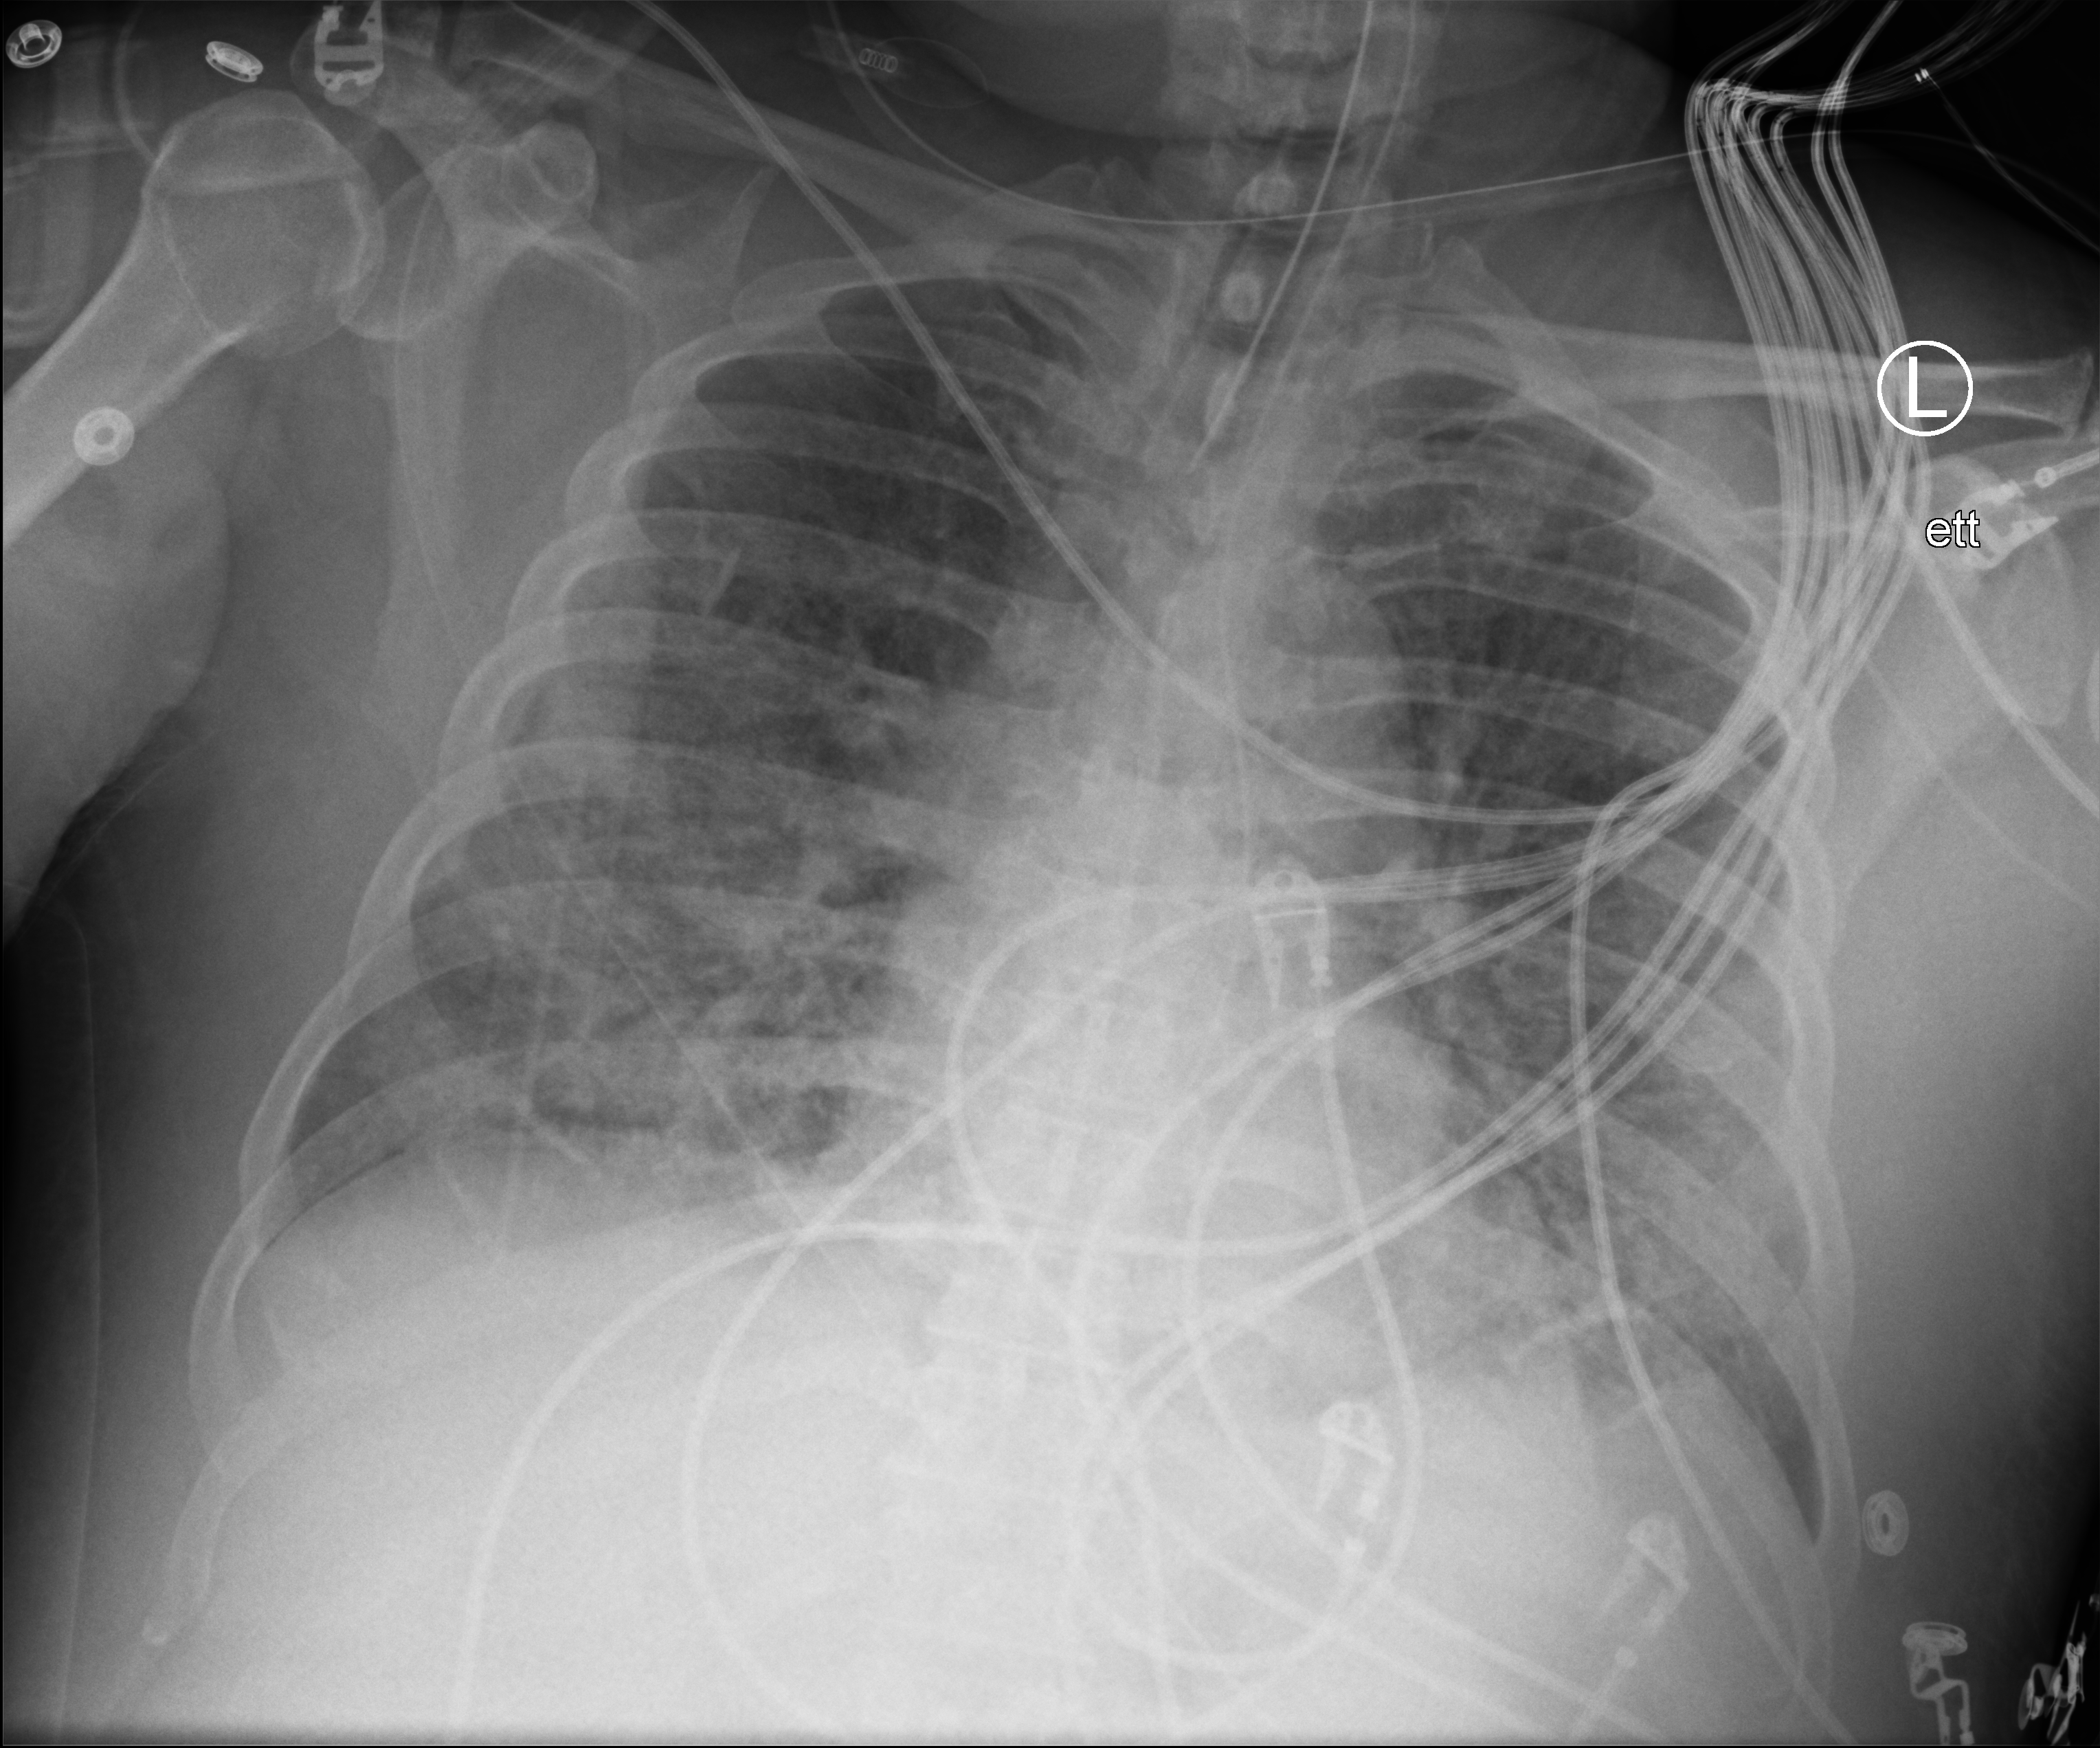
Bedside chest radiograph (computed radiography), anteroposterior (AP) projection. Male patient hospitalised with COVID-19, age 60–74 years.
Admission-level facts for this patient (not findings on this image; timing relative to this image not recorded): mechanically ventilated during this hospital stay: yes; admitted to intensive care during this hospital stay: yes; chronic kidney disease (admission record): no.